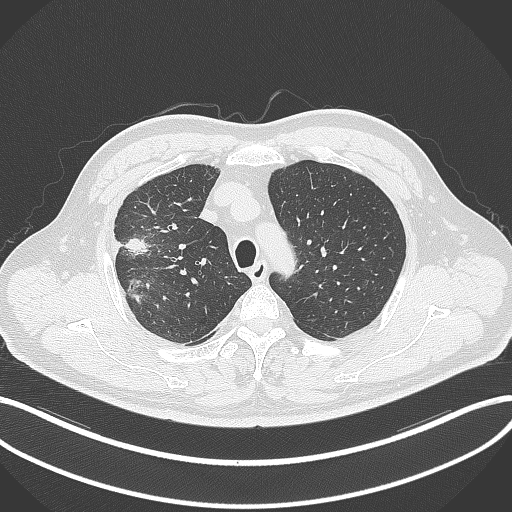
Chest CT, one axial slice; position 268 of 348 along the scan axis; lung window (W 1500 / L -600 HU); 1 mm slice thickness; 512 × 512 image matrix, field of view 400 × 400 mm. Male patient, age 55 years. From the clinical record (not read from this slice): clinical TNM (as recorded): T3 N2 M1.
Annotated regions visible in this slice (rectangle marked by the reading radiologist):
- lung tumour (recorded histology: adenocarcinoma): bounding box (x1, y1, x2, y2) in pixels: (121, 235, 159, 306)